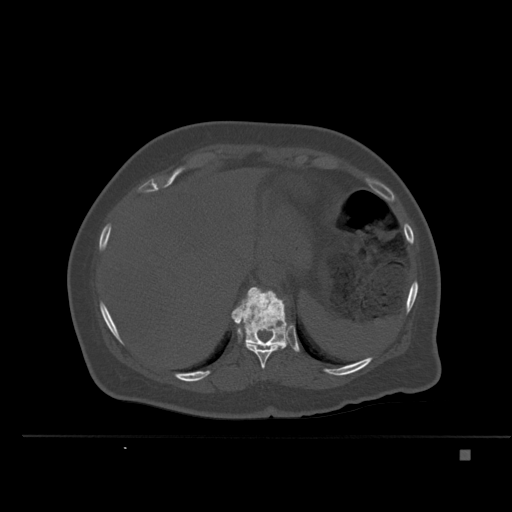
CT including the spine, one axial slice; position 275 of 477 along the scan axis; bone window (W 1800 / L 400 HU); 512 × 512 image matrix, field of view 422 × 422 mm. Female patient, age 74 years. From the clinical record (not read from this slice): primary cancer: colon.
Outlined on this slice (semi-automatic segmentation, software-assisted and operator-edited):
- T10 vertebra: bounding box (x1, y1, x2, y2) in pixels: (244, 341, 280, 369)
- T11 vertebra: (231, 287, 288, 349)